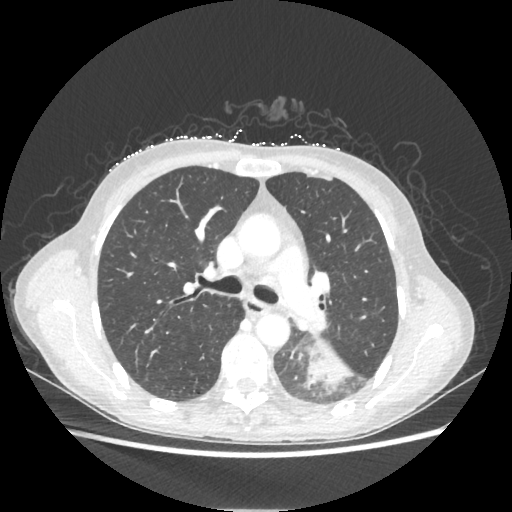
Chest CT, one axial slice. Slice 135 of 221 in the series (ordered by position). Reconstruction kernel STANDARD. 80 kVp. Lung window (W 1500 / L -600 HU). 1.25 mm slice thickness. 512 × 512 image matrix, field of view 360 × 360 mm. Patient: female, 53 years. From the clinical record (not read from this slice): clinical TNM (as recorded): T3 N0 M0.
Outlined on this slice (bounding box drawn by a radiologist):
- lung tumour (recorded histology: adenocarcinoma): box from (x=305, y=339) to (x=353, y=389) px